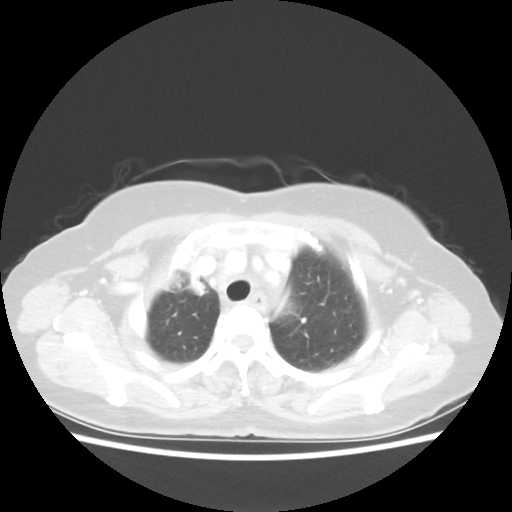
Chest CT, one axial slice. Slice 44 of 55 in the series (ordered by position). Reconstruction kernel STANDARD. 80 kVp. Lung window (W 1500 / L -600 HU). 5 mm slice thickness. 512 × 512 image matrix, field of view 337 × 337 mm. Female patient, age 62 years. From the clinical record (not read from this slice): clinical TNM (as recorded): T4 N3 M0.
Annotated regions visible in this slice (bounding box drawn by a radiologist):
- lung tumour (recorded histology: squamous cell carcinoma): bounding box [x1, y1, x2, y2] px = [155, 257, 211, 298]